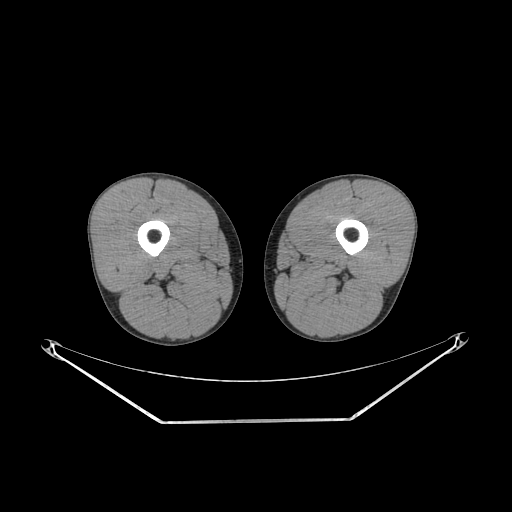
CT of an extremity soft-tissue mass (from a PET/CT study), one axial slice. Position 213 of 267 along the scan axis. Soft-tissue window (W 400 / L 40 HU). 512 × 512 image matrix, field of view 500 × 500 mm. Male patient. Case-level facts recorded for this patient, not image findings: histological type: extraskeletal osteosarcoma; grade: high; site of the primary tumour: left adductur.
Annotated regions visible in this slice (expert contour drawn on MRI and transferred to this co-registered scan by the dataset authors):
- gross tumour volume (mass): box from (x=331, y=256) to (x=348, y=268) px